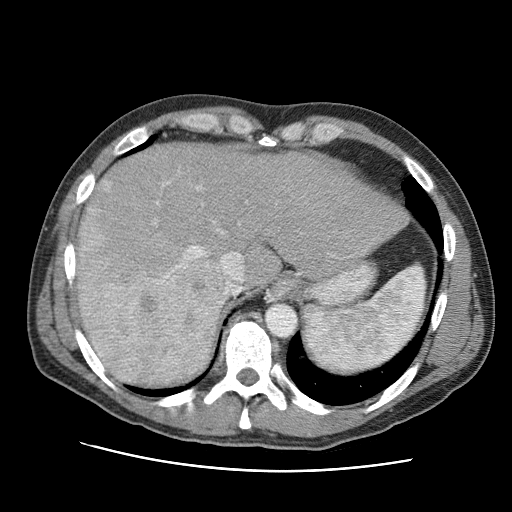
Contrast-enhanced abdominal CT (liver protocol), one axial slice. Position 75 of 95 along the scan axis. Reconstruction kernel STANDARD. 120 kVp. One of 2 acquisitions stored at this slice position. Soft-tissue window (W 400 / L 40 HU). 2.5 mm slice thickness. 512 × 512 image matrix, field of view 360 × 360 mm. Case-level facts recorded for this patient, not image findings: diagnosis: hepatocellular carcinoma (patient treated with transarterial chemoembolisation; whether this scan precedes or follows treatment is not stated here); TNM stage (as recorded): Stage-IVA; Child-Pugh class: A; tumour differentiation: moderately differentiated; tumour nodularity: multinodular.
Annotated regions visible in this slice (semi-automatically segmented with operator editing):
- liver parenchyma outside the tumour (the mass and vessels are separate outlines, so this box may not span the whole liver): bounding box [x1, y1, x2, y2] px = [76, 144, 408, 368]
- mass: [75, 174, 230, 388]
- liver vessels: [157, 181, 244, 294]